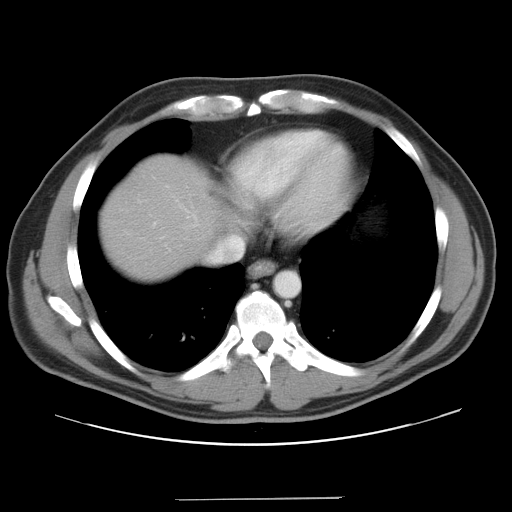
Contrast-enhanced abdominal CT, one axial slice; position 35 of 37 along the scan axis; reconstruction kernel STANDARD; soft-tissue window (W 400 / L 40 HU); 512 × 512 image matrix. Male patient, age 46 years. Case-level facts recorded for this patient, not image findings: diagnosis: colorectal cancer liver metastases, imaged before liver resection; multiple liver metastases: yes; largest metastasis: 1 cm; disease in both lobes: no.
Annotated regions visible in this slice (manually delineated by an expert):
- hepatic veins: bounding box (x1, y1, x2, y2) in pixels: (210, 235, 244, 262)
- liver: (102, 159, 214, 276)
- planned liver remnant (the part of the liver to remain after resection): (102, 159, 214, 275)